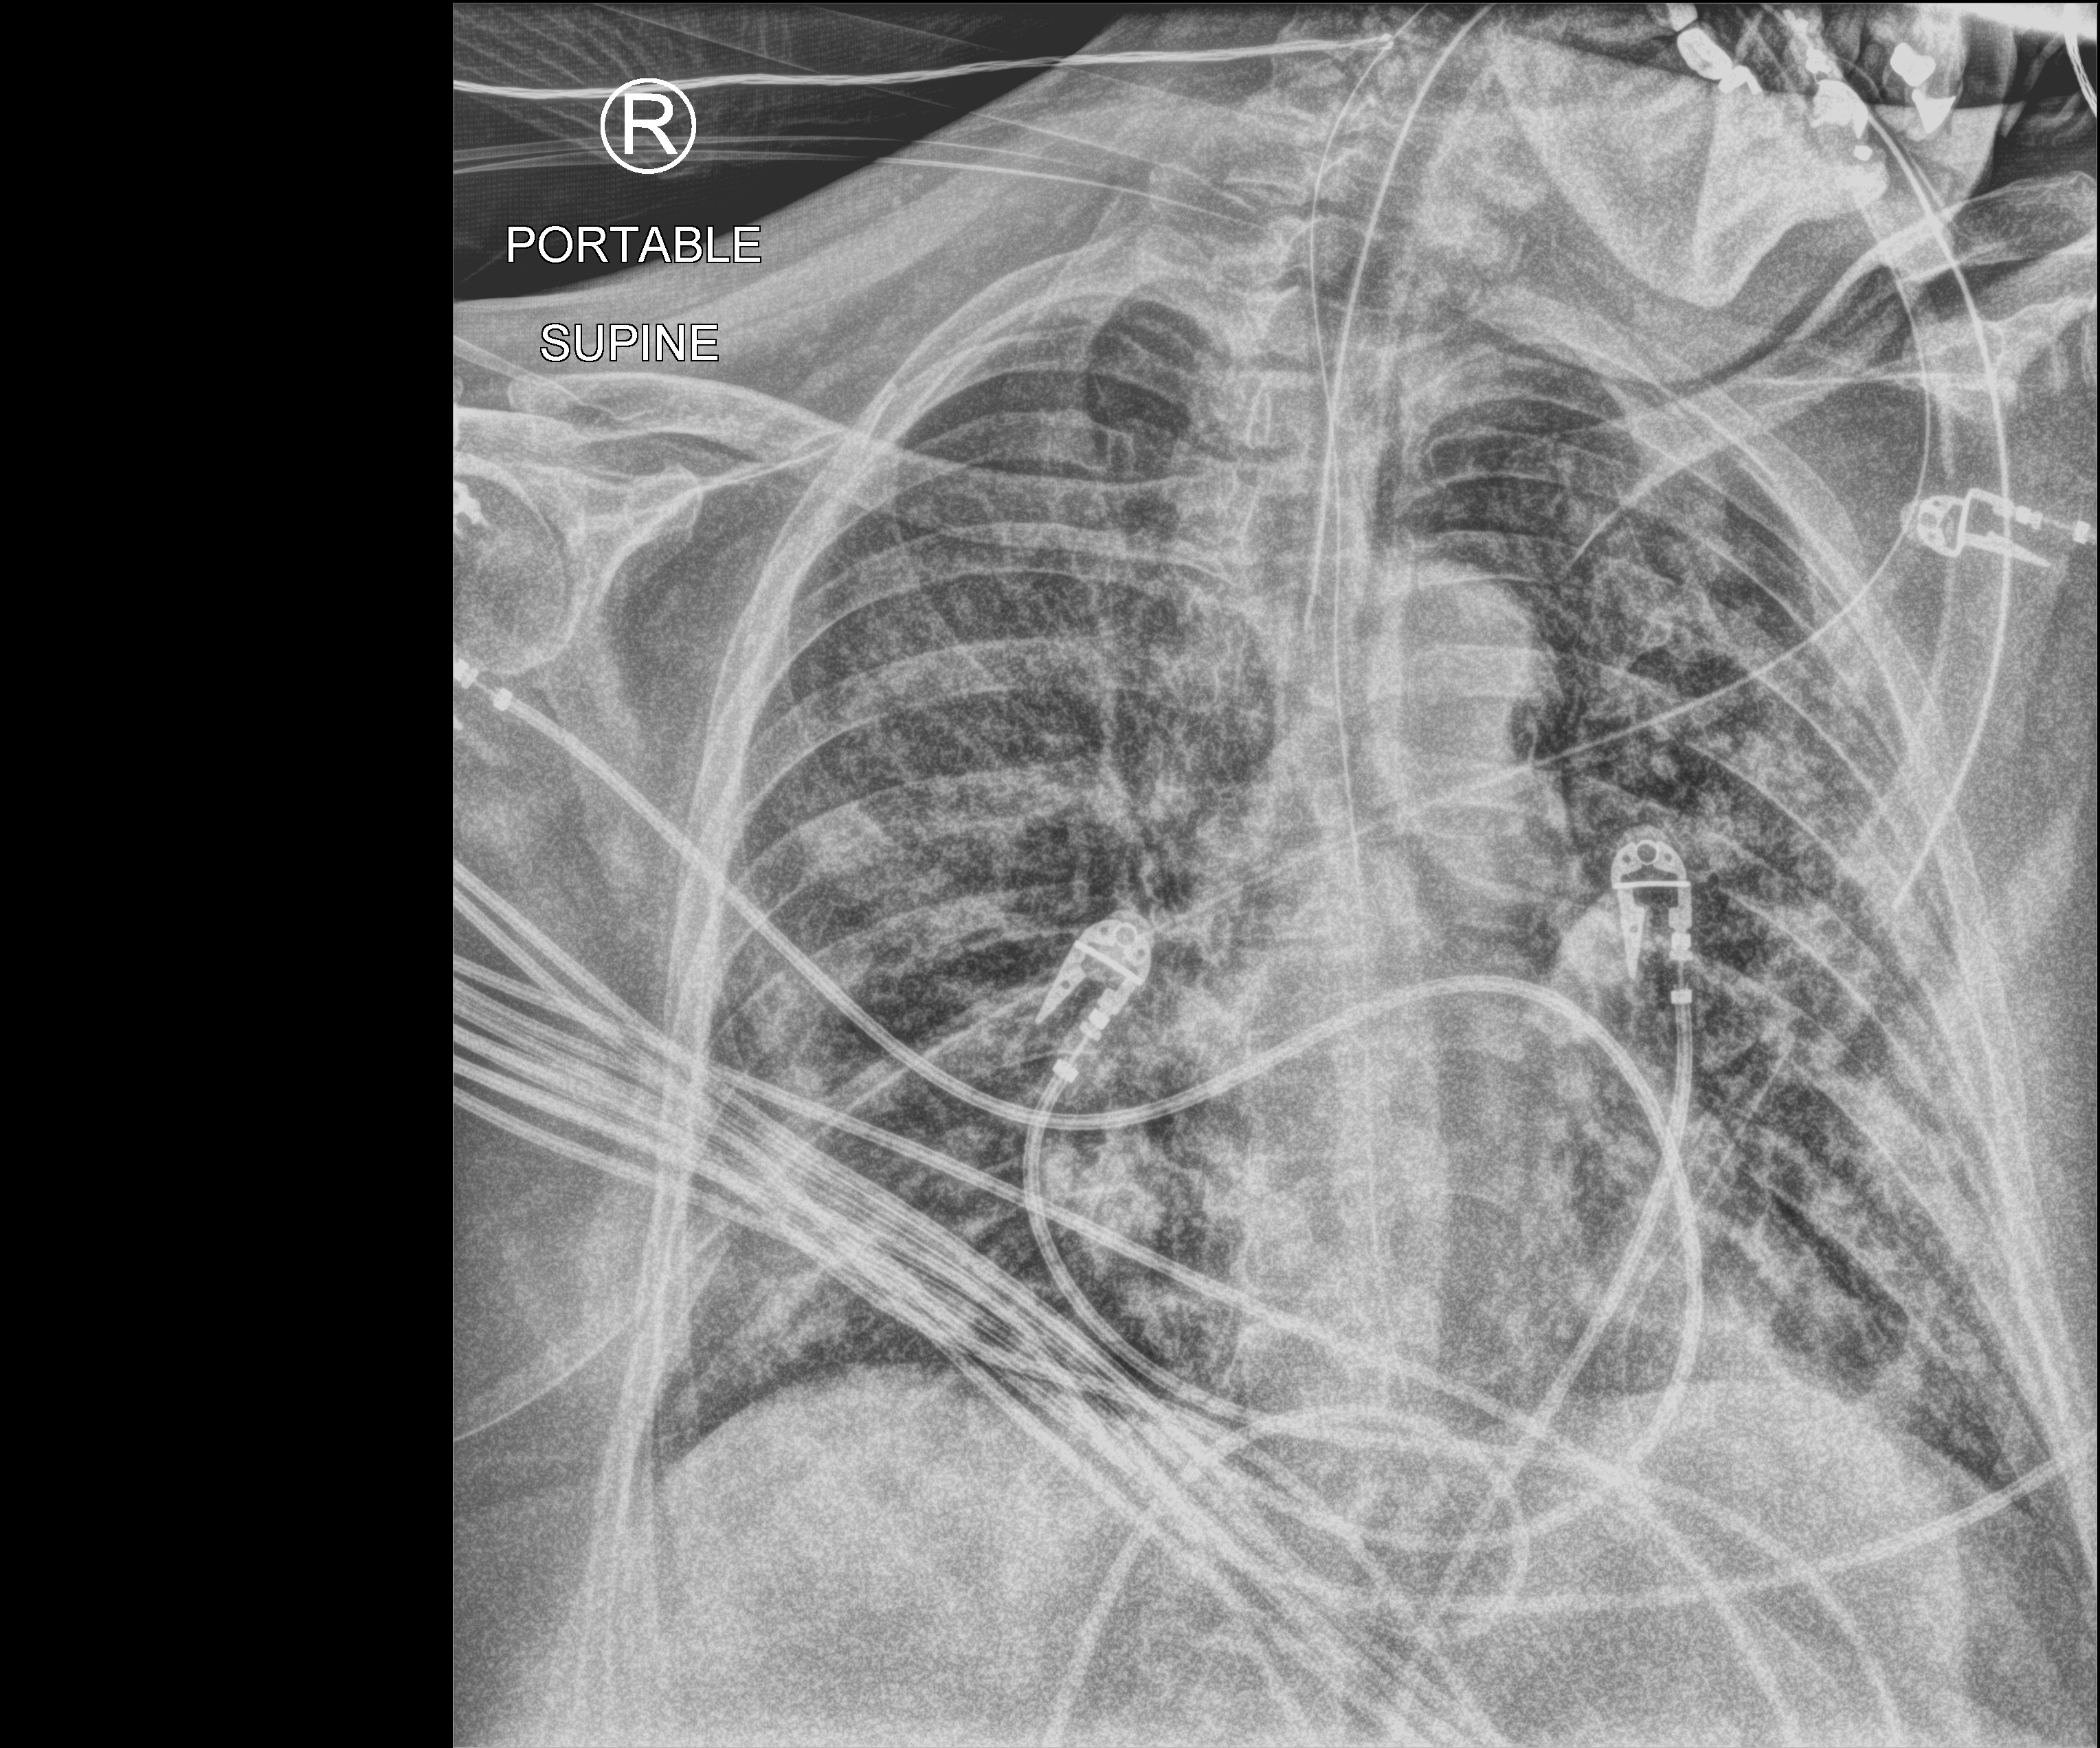
Portable chest radiograph; anteroposterior (AP) projection. Patient hospitalised with COVID-19; female, aged 60–74 years.
From the hospital-stay record, not from the radiograph (when in the stay this image was taken is not recorded):
- admitted to intensive care during this hospital stay: yes